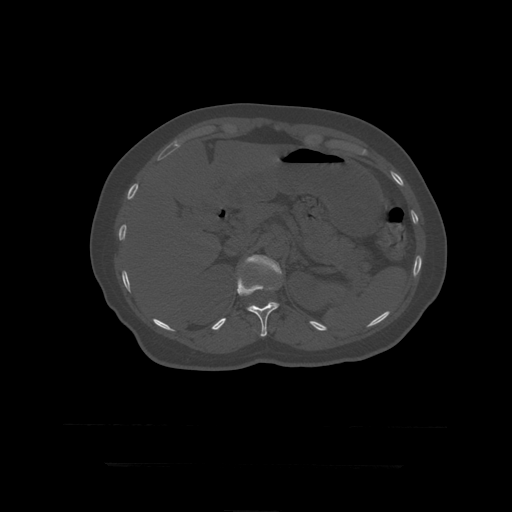
CT including the spine, one axial slice. 120 kVp. Bone window (W 1800 / L 400 HU). 1.25 mm slice thickness. 512 × 512 image matrix. Patient age 41 years. From the clinical record (not read from this slice): primary cancer: breast.
Structures marked on this image (semi-automatically segmented with operator editing):
- L1 vertebra: bounding box <244,255,283,307> (left, top, right, bottom; pixels)
- T12 vertebra: <237,271,281,337>